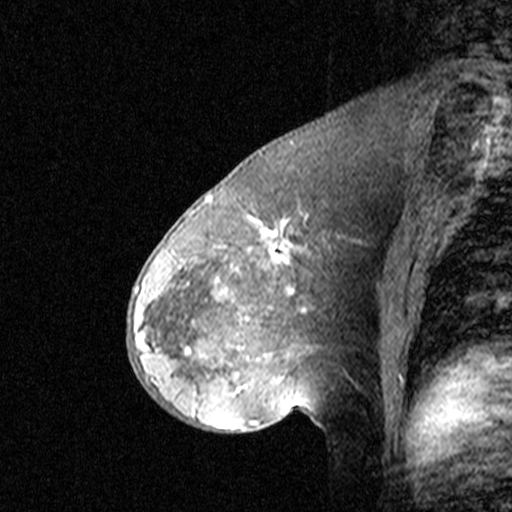
Breast MRI (dynamic contrast-enhanced), one sagittal slice. Slice 23 of 44 in the series (ordered by position). Dynamic contrast-enhanced study with each time point stored as its own series, time point 2 of 3 at this slice position (early post-contrast, ordered by acquisition time). 1.5 T. TE 4.5 ms, TR 11 ms. 3 mm slice thickness. 512 × 512 image matrix, field of view 200 × 200 mm. Female patient, age 46 years. Case-level facts recorded for this patient, not image findings: setting: breast cancer imaged before/during neoadjuvant chemotherapy; receptor status: HER2-positive.
Annotated regions visible in this slice (semi-automatic segmentation, software-assisted and operator-edited):
- analysis volume of interest (the breast-tissue region the enhancement analysis was run in; not a lesion): bounding box [x1, y1, x2, y2] px = [144, 172, 359, 393]
- tumour enhancement mask (voxels above the 90 % enhancement threshold inside the analysis volume of interest): [144, 197, 340, 393]